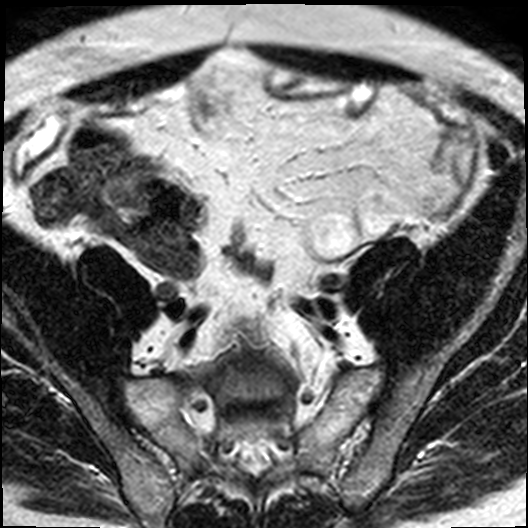
Multiparametric prostate MRI examination; 3 images, each a single mid-volume slice chosen by position (not for content). Treatment context recorded for this patient: Surgery.
Image 1: axial T2-weighted image, series "T2W_TSE_AX", slice 21 of 40.
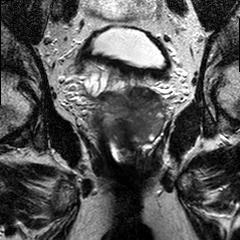
Image 2: T2-weighted coronal slice, slice 16 of 30.
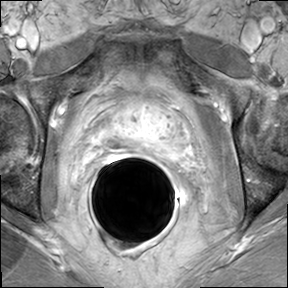
Image 3: DCE (dynamic gadolinium-enhanced) axial slice, series "AX BLISS_GAD_8", slice 18 of 34, dynamic phase 5 of 8, 6 mm slice thickness.
MRI report (verbatim):
FINDINGS: The prostate has a maximal lateral diameter of 5.4 cm, a maximal craniocaudal diameter of 4.8 cm and a maximal AP diameter of 3.1 cm resulting in an estimated gland volume of 42 cc. There is marked BPH present; there is also a prominent 3.0 x 3.1 cm middle lobe present with protrusion into the bladder neck. The zonal anatomy is preserved. In the midthird of the prostate within the lateral and posterior lateral left peripheral zone there is a geographic area of T2-weighted hypo- intense signal with partial rapid wash in and wash out kinetics on the dynamic series; the dominant nodule within the left posterior lateral peripheral zone measures approximately 2 x 1 cm. In the right posterior lateral peripheral zone of the lower mid third/apical third of the prostate there is a second dominant nodule seen in measuring 8 x 9 mm, with suspicious wash in and wash out genetics on the dynamic series and nodular T2-weighted hypointense signal, similar to the nodule in the left peripheral zone. In addition, there are several small areas of diffuse hypointense signal alteration on the T2-weighted images with abnormal kinetics seen,
mostly in the left peripheral zone of base midthird and apical third, and to a lesser extent in the right peripheral zone, within areas of hemorrhagic changes caused by the recent biopsy. There is no evidence of manifest extra-capsular extension or seminal vesicle infiltration. The neurovascular bundles seem not to be involved on either side. There are no suspicious the enlarged obturator or iliac lymph nodes seen on either side. Multiplanar reconstructions, subtraction images, and CAD analysis of the dynamic series for assessment of the kinetic information facilitated the interpretation of the exam. IMPRESSION: Bilateral prostate cancer with left sided dominance, without evidence of extraglandular disease, as detailed above. No MRI evidence of neurovascular bundle involvement on either side. No seminal vesicles involvement. No pelvic lymphadenopathy. Marked BPH with prominent middle lobe.

Biopsy pathology report for this patient (as recorded):
The specimen consists of multiple brown/tan core biopsies measuring in length from 0.3 cm up to 2 cm and 0.01 cm in diameter each. The specimen is submitted in toto in six cassettes as follows: 1 right PZ, 2 right PZ/TZ, 3 right apex, 4 left PZ, 5 left PZ/TZ, 6 left apex. PROSTATIC CORE NEEDLE BIOPSIES:
1. RIGHT PZ PROSTATIC ADENOCARCINOMA, GLEASON SCORE (3+3)=6/10, INVOLVING APPROXIMATELY 15% OF TISSUE REPRESENTED.
2. RIGHT PZ/TZ PROSTATIC ADENOCARCINOMA, GLEASON SCORE (3+4) =7/10, INVOLVING APPROXIMATELY 40% OF TISSUE REPRESENTED.
3. RIGHT APEX PROSTATIC ADENOCARCINOMA, GLEASON SCORE (3+3) =6/10, INVOLVING APPROXIMATELY 30% OF TISSUE REPRESENTED.
4. LEFT PZ PROSTATIC ADENOCARCINOMA, GLEASON SCORE (3+4) =7/10, INVOLVING APPROXIMATELY 30% OF TISSUE REPRESENTED.
5. LEFT PZ/TZ: PROSTATIC ADENOCARCINOMA, GLEASON SCORE (3+4) =7/10, INVOLVING APPROXIMATELY 40% OF TISSUE REPRESENTED.
6. LEFT APEX PROSTATIC ADENOCARCINOMA, GLEASON SCORE (3+4) =7/10, INVOLVING APPROXIMATELY 10% OF TISSUE REPRESENTED.